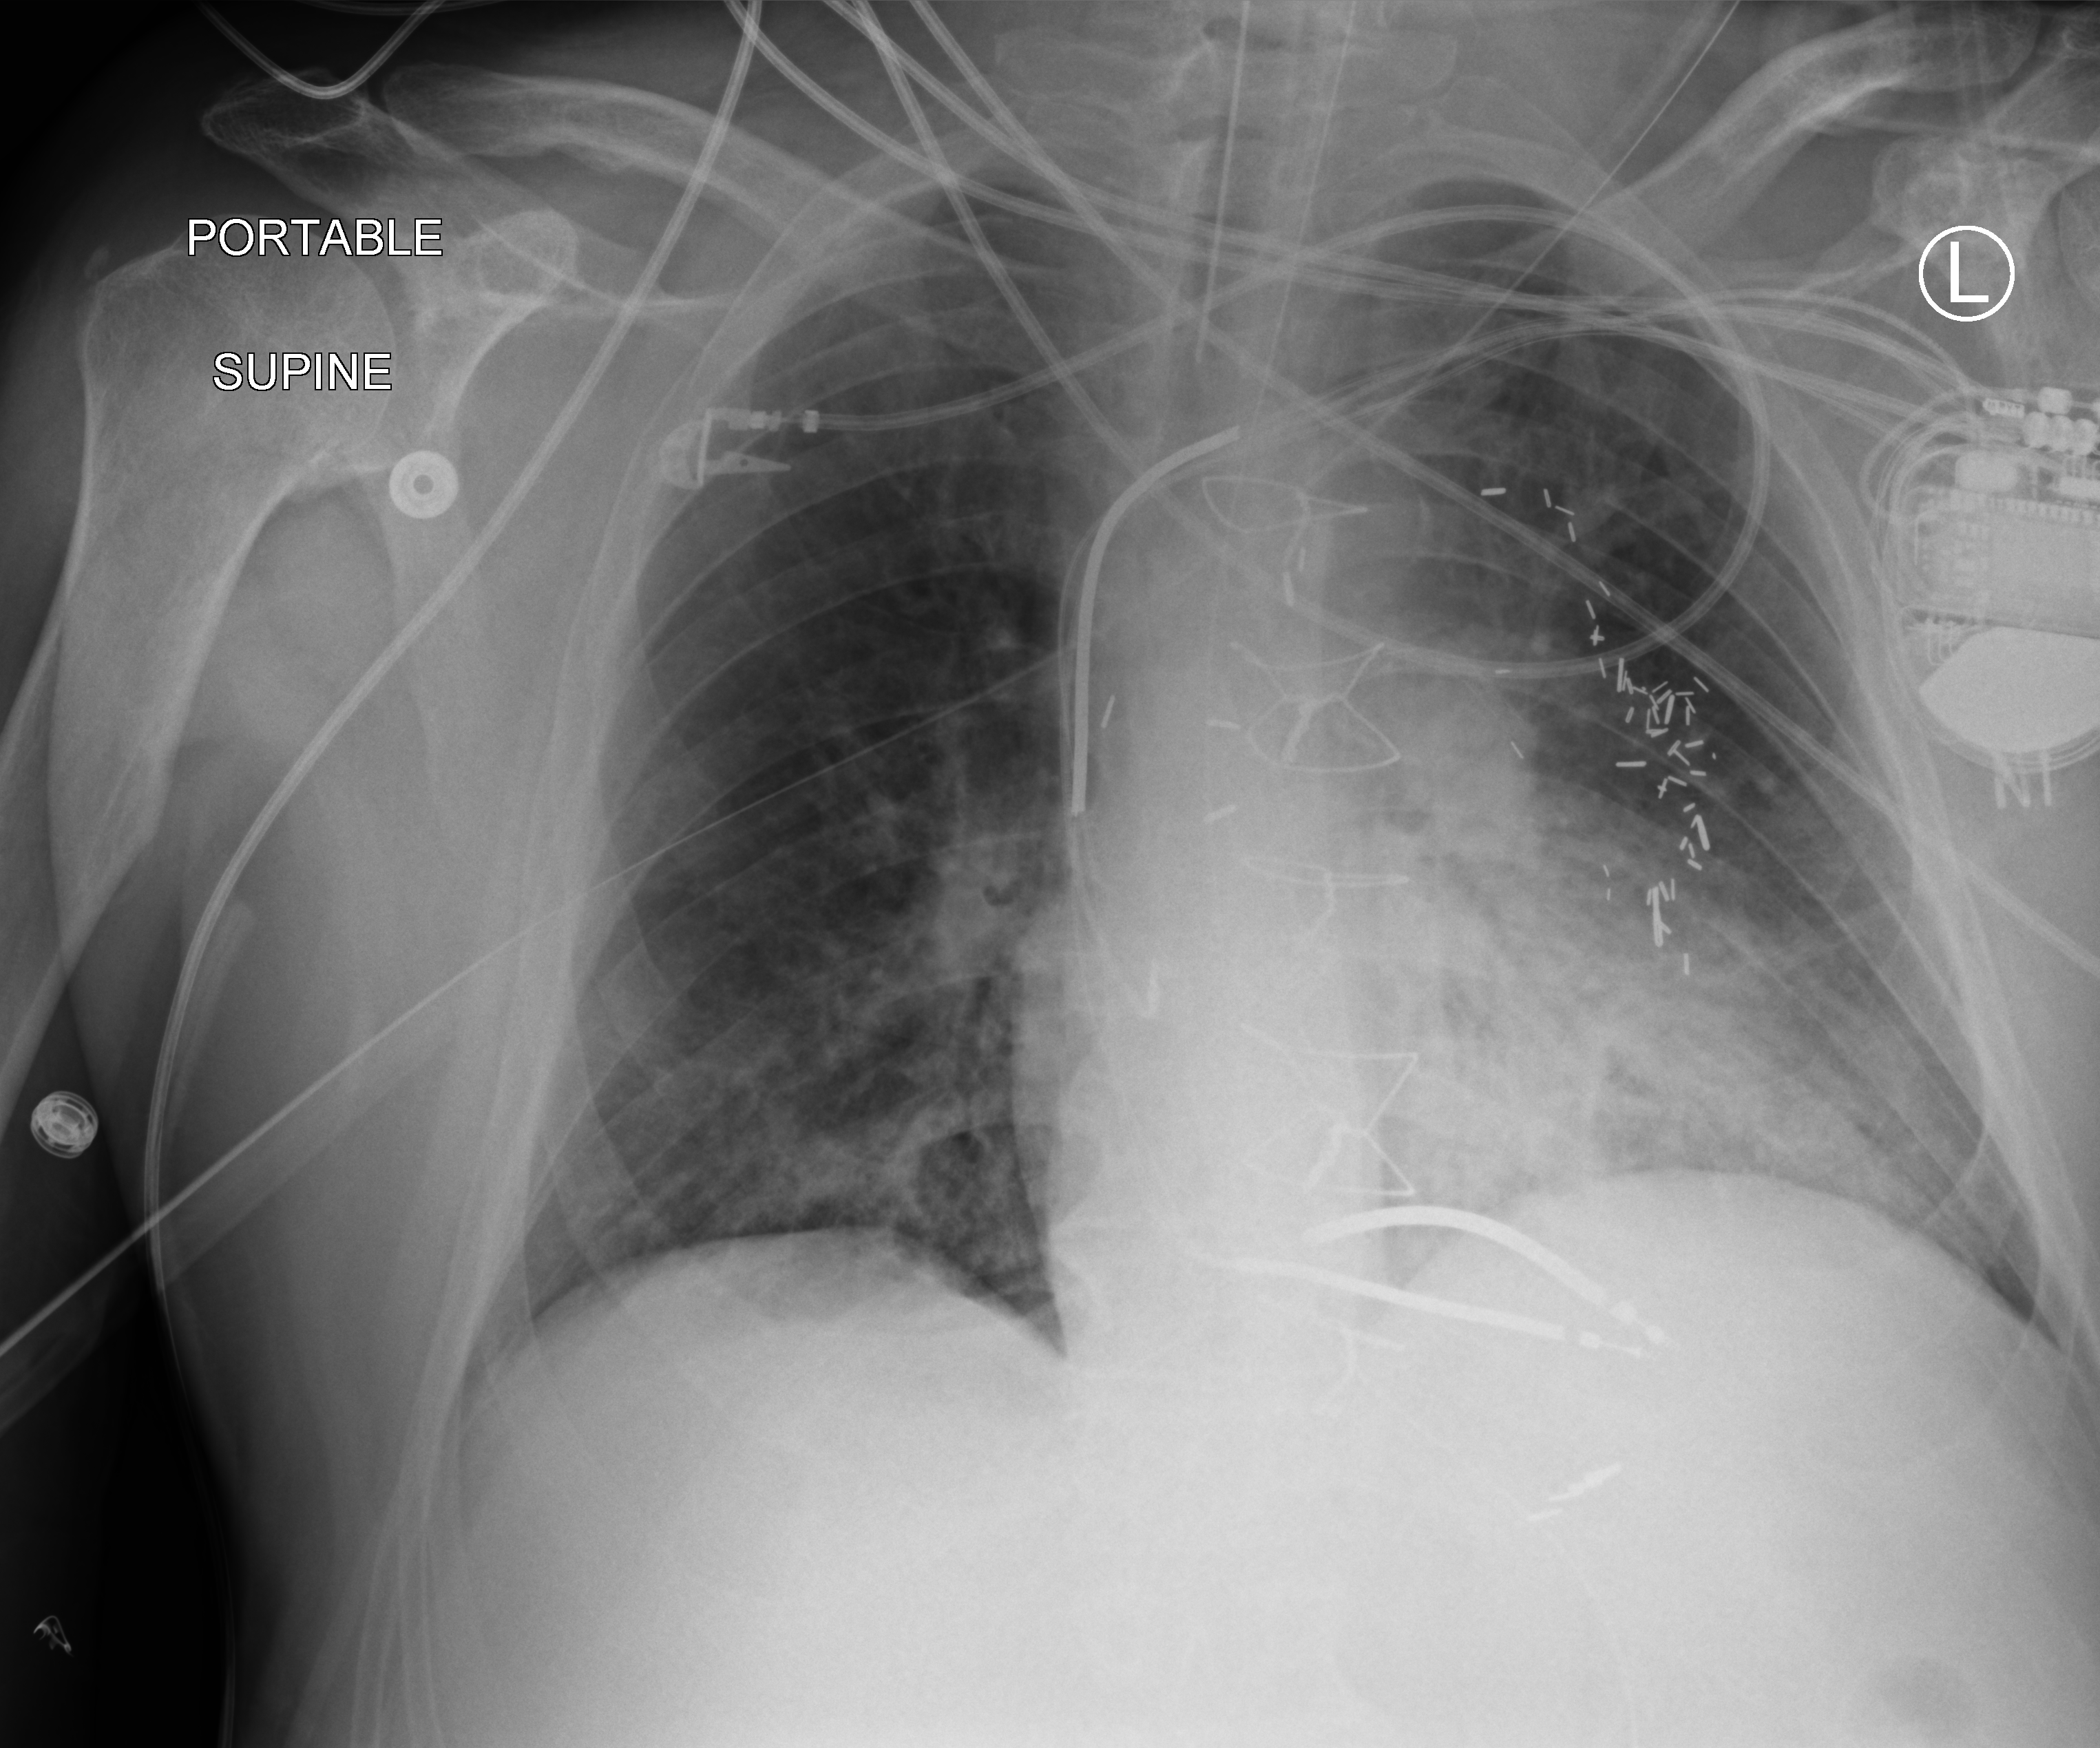
Portable chest radiograph, anteroposterior (AP) projection. Patient hospitalised with COVID-19; male, aged 60–74 years.
Admission-level facts for this patient (not findings on this image; timing relative to this image not recorded):
- COPD (admission record): no
- admitted to intensive care during this hospital stay: yes
- mechanically ventilated during this hospital stay: yes